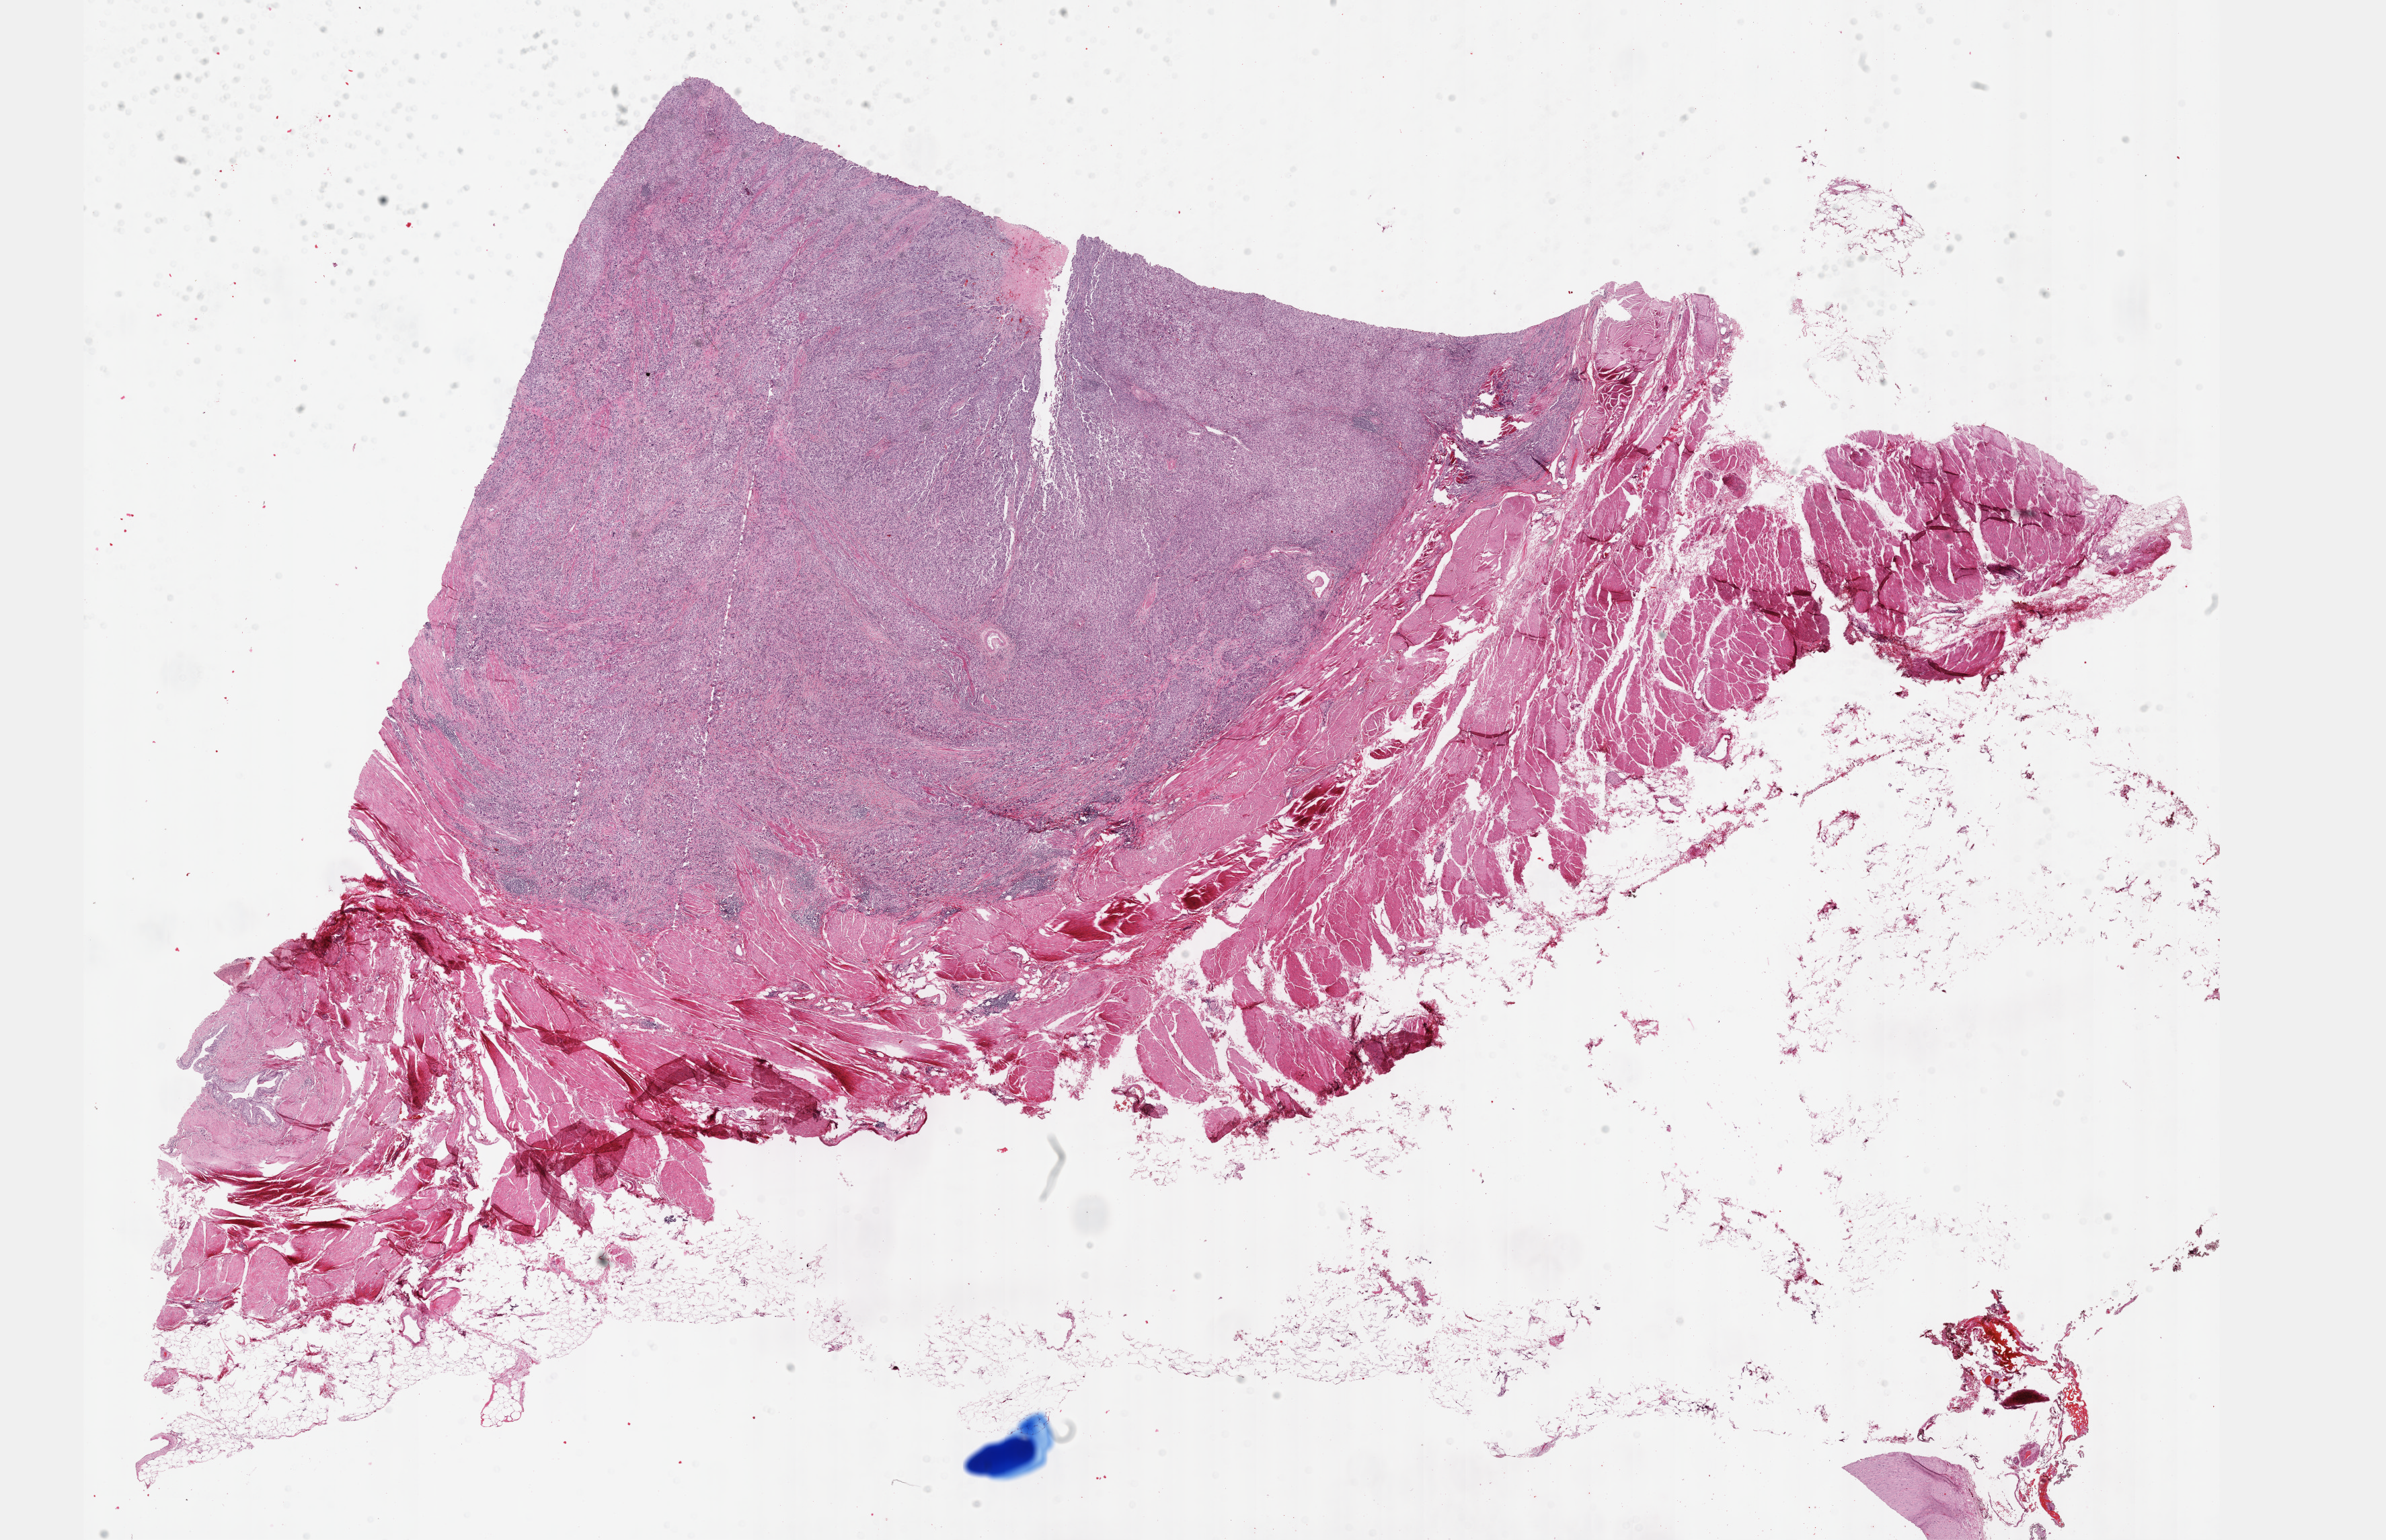
Digitized H&E tissue section (whole slide), whole scanned area (about 28.7 x 18.5 mm, acquisition: 40x scan) shown as a low-resolution overview. FFPE section. Sample: primary tumour, bladder. Male, age 83 years at initial diagnosis. Histologic grade: high grade.
AJCC pathologic stage: IV (7th edition). Histologic diagnosis: Transitional cell carcinoma.